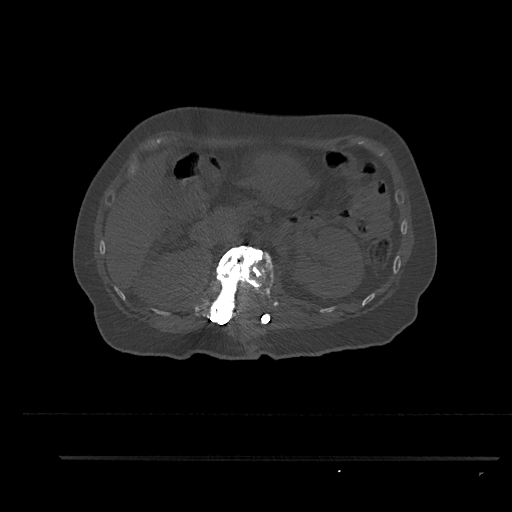
CT including the spine, one axial slice. Position 221 of 797 along the scan axis. Reconstruction kernel Br40s/3. Bone window (W 1800 / L 400 HU). 0.5 mm slice thickness. 512 × 512 image matrix. Patient: female, 44 years. Case-level facts recorded for this patient, not image findings: primary cancer: renal; vertebrae with lytic lesions (as recorded): L1.
Outlined on this slice (semi-automatic segmentation, software-assisted and operator-edited):
- L1 vertebra: bounding box (x1, y1, x2, y2) in pixels: (207, 246, 275, 322)